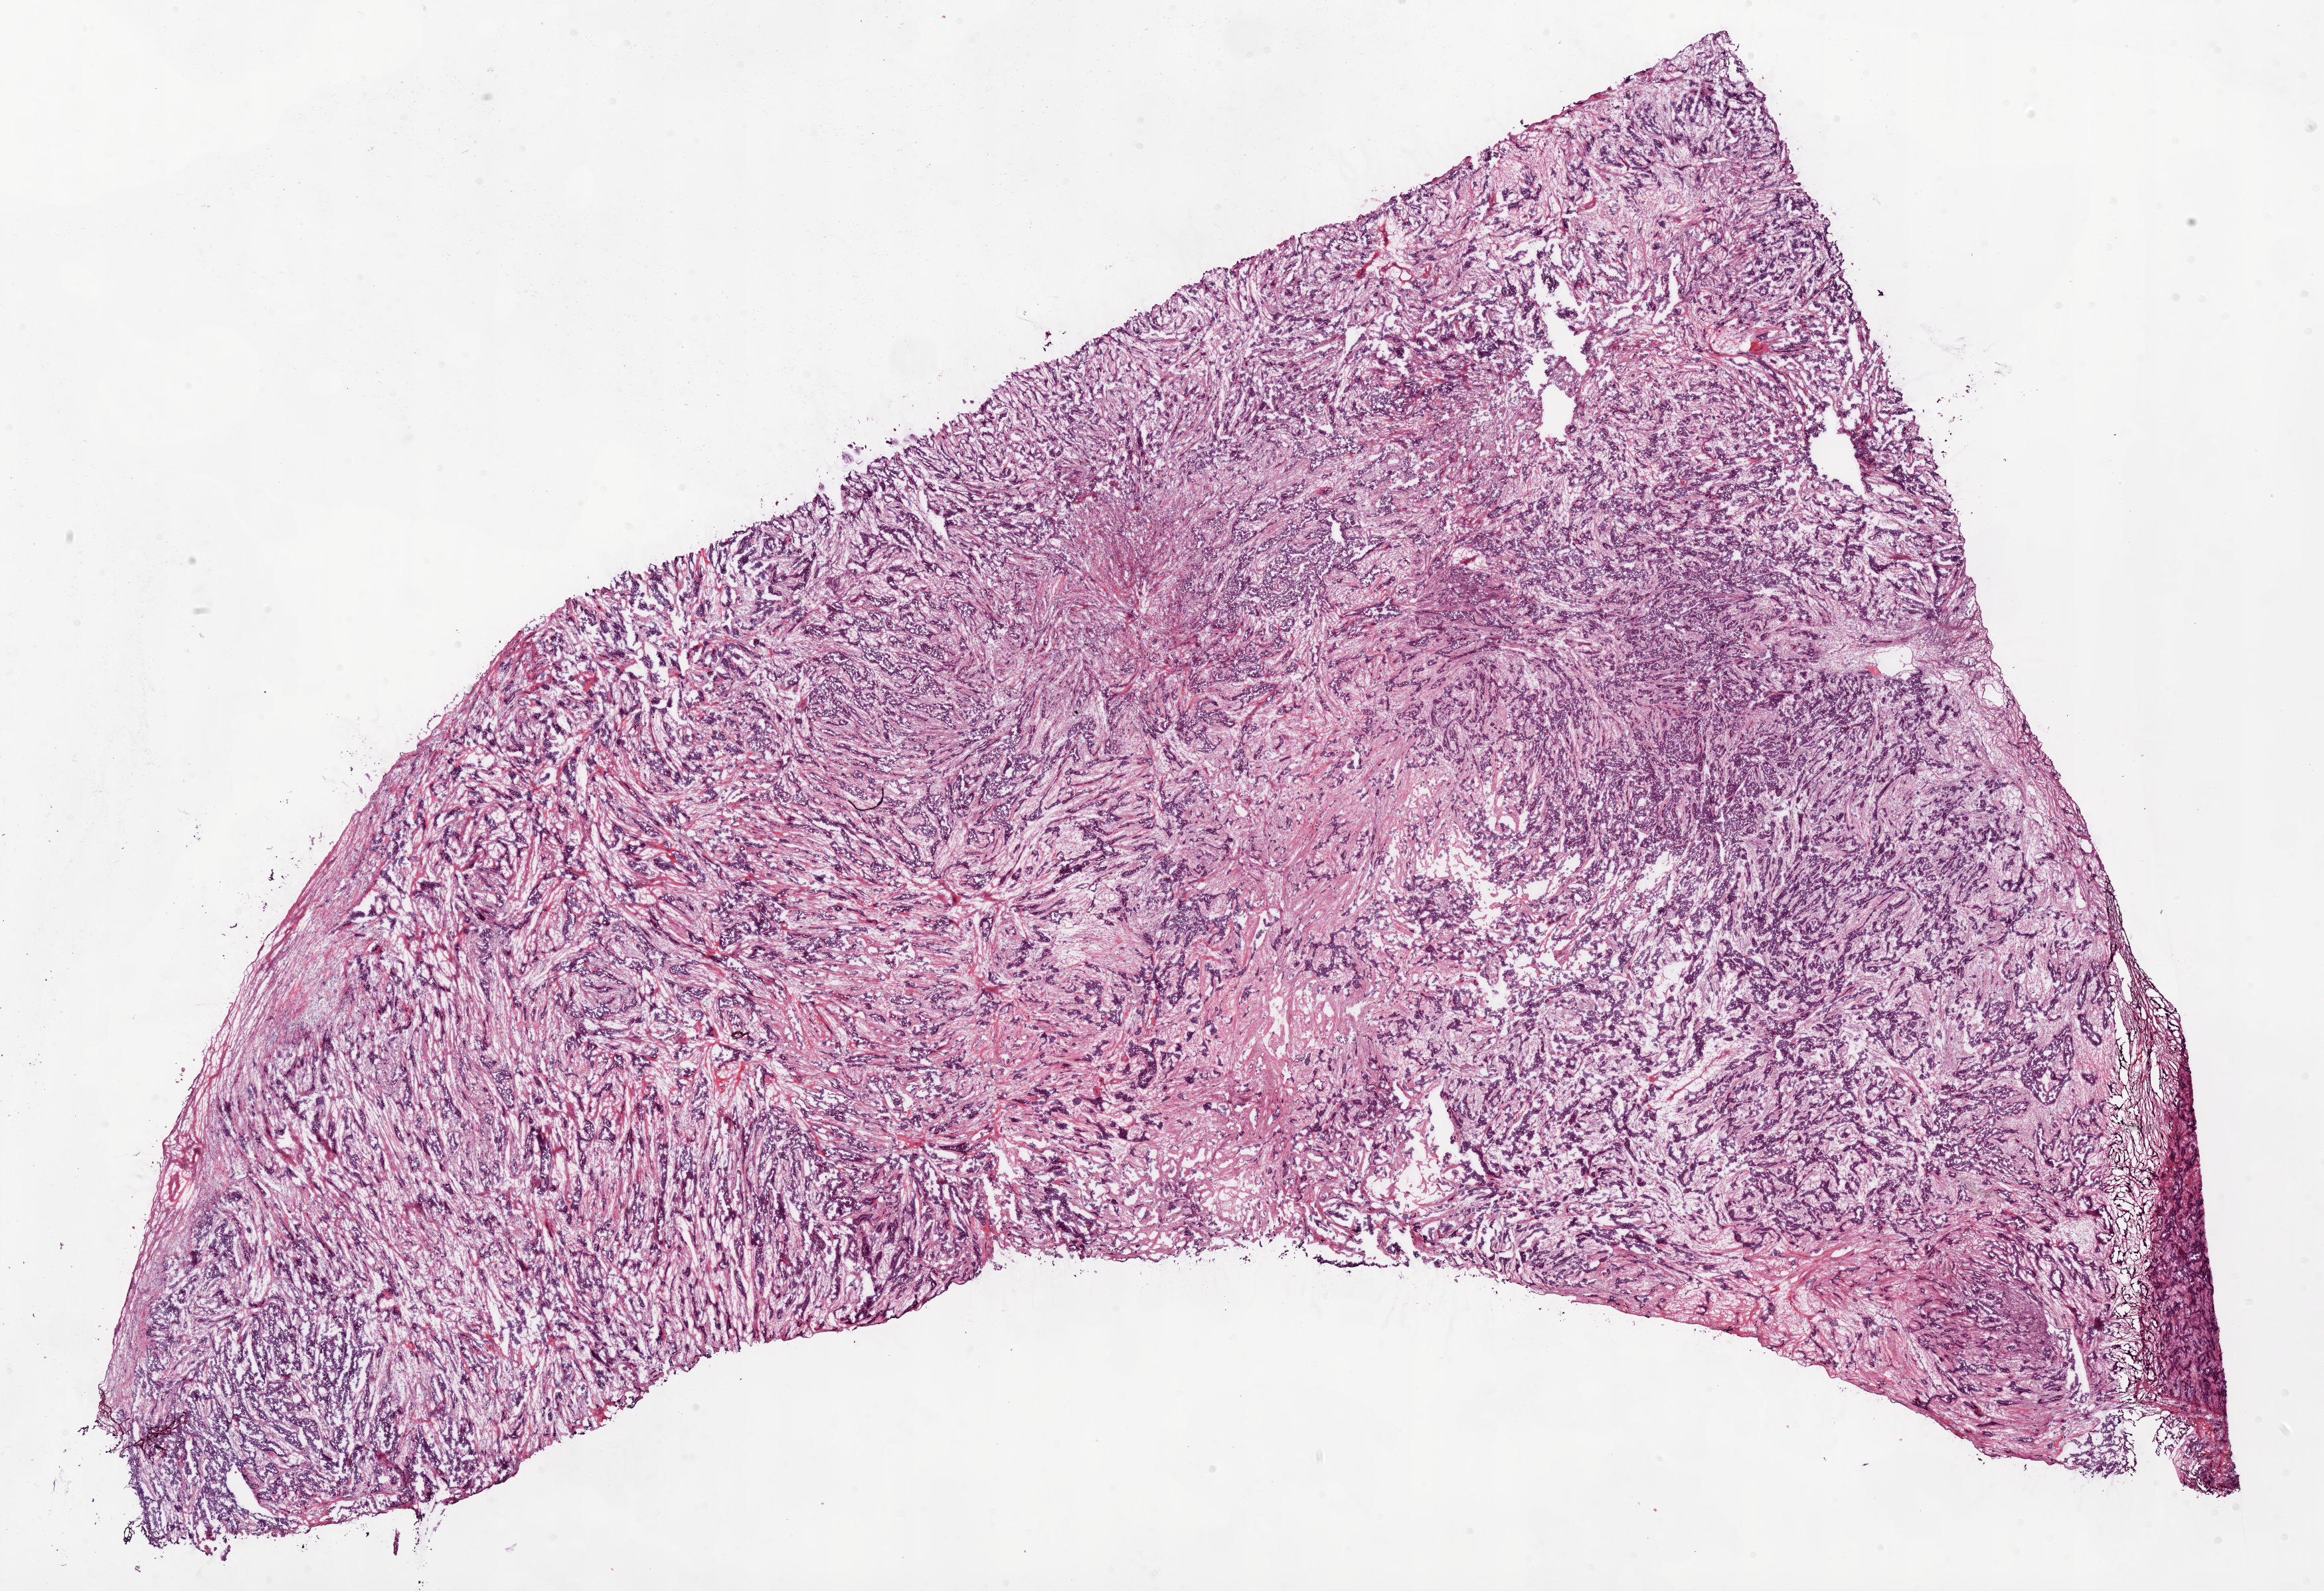
Whole-slide histology image, H&E-stained, whole scanned area (about 28.1 x 19.2 mm) shown as a low-resolution overview. Frozen section. Ovary, primary tumour sample. Patient: female, age at initial diagnosis 59 years. Histologic grade: G3 (poorly differentiated). Slide review estimates, as recorded: tumour cells 50%, tumour nuclei 90%, normal cells 0%, stromal cells 50%, necrosis 0%. Inflammatory infiltration, as recorded: lymphocyte infiltration 0%, monocyte infiltration 0%, neutrophil infiltration 0%.
Pathologic diagnosis: Serous cystadenocarcinoma, NOS. FIGO stage: IIIC.